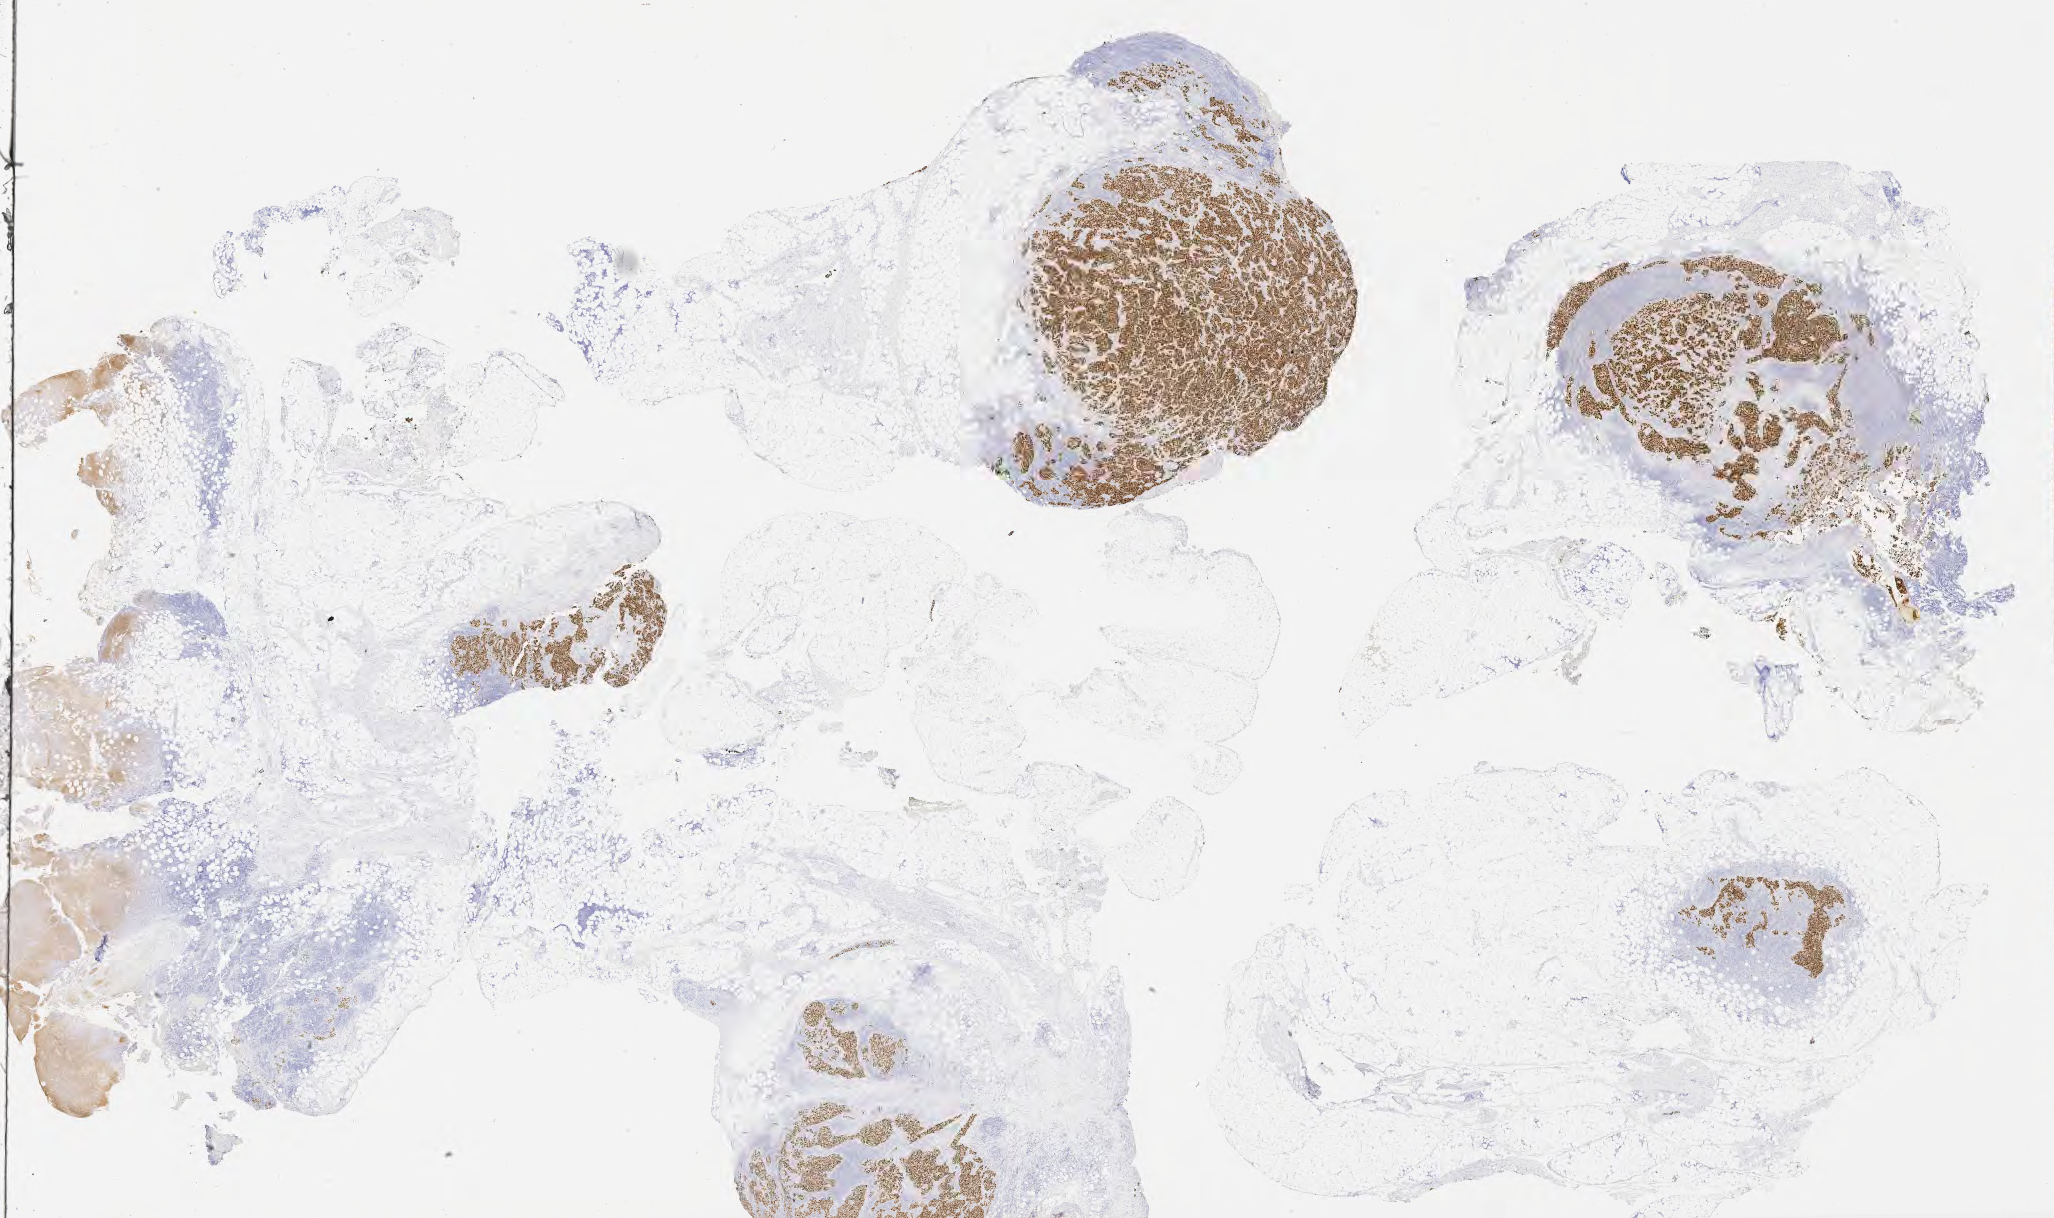
Whole-slide image, immunohistochemical stain for TTF-1 (thyroid transcription factor 1) — a low-resolution overview of the entire scanned area, about 33.2 x 19.7 mm, specimen: tumor tissue, site: lung. Patient: male, aged 58.
Diagnosis: Adenocarcinoma, NOS.